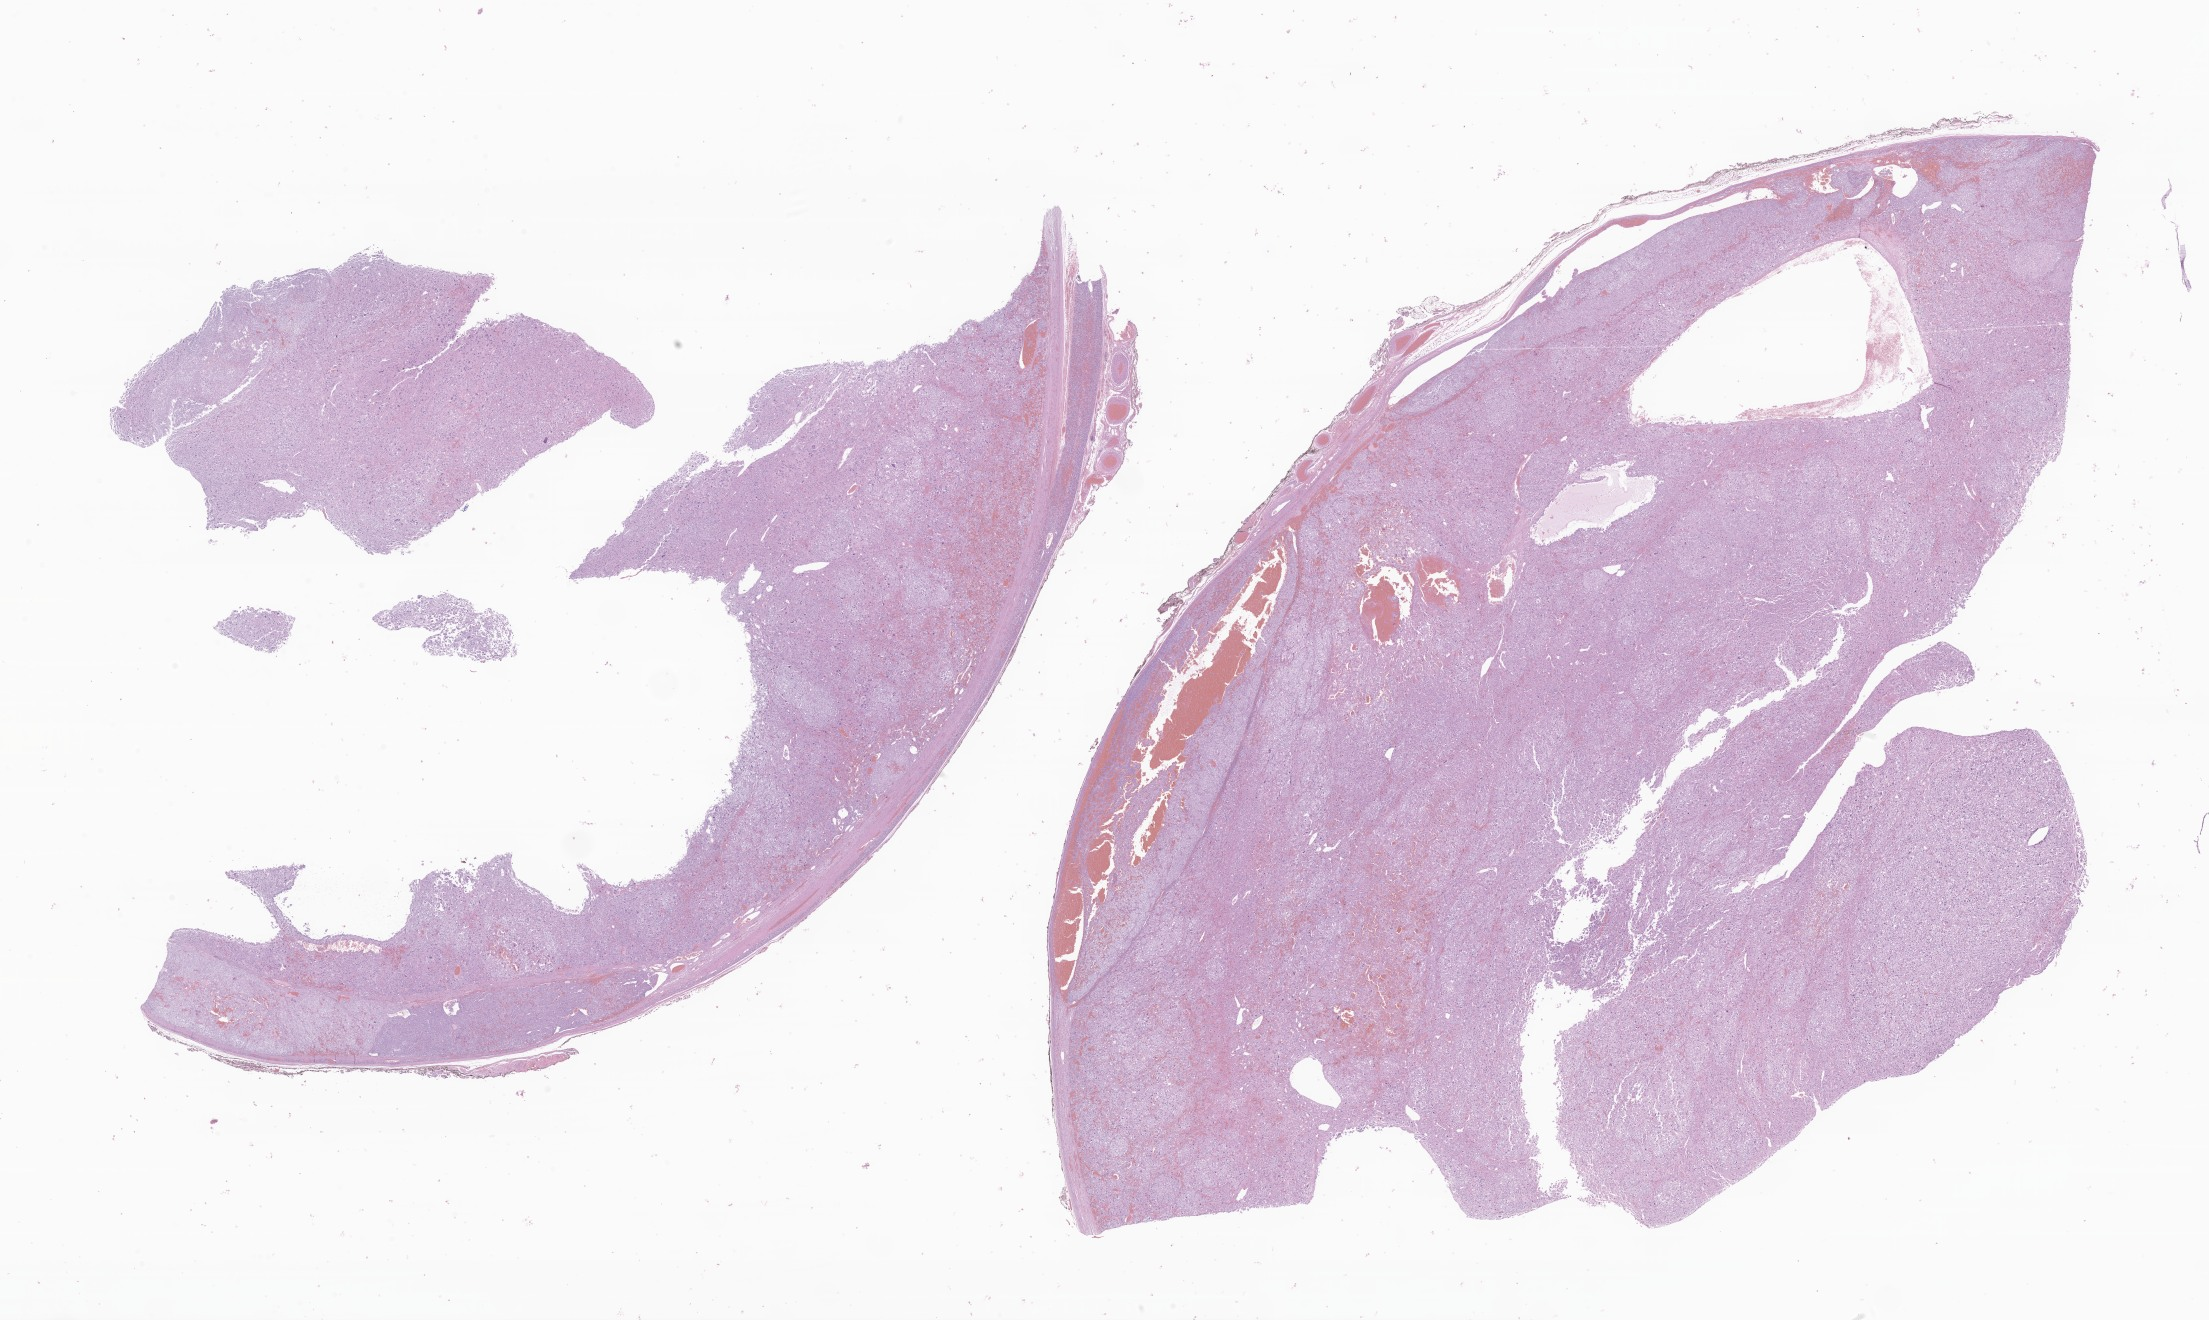
Whole-slide image, H&E stain of tumor tissue from the adrenal gland, low-resolution overview of the scanned area, about 37.3 x 22.3 mm, formalin-fixed, paraffin-embedded (FFPE) tissue. Patient male; age 46 months (3 years 10 months).
• recorded diagnosis: Adrenal cortical carcinoma